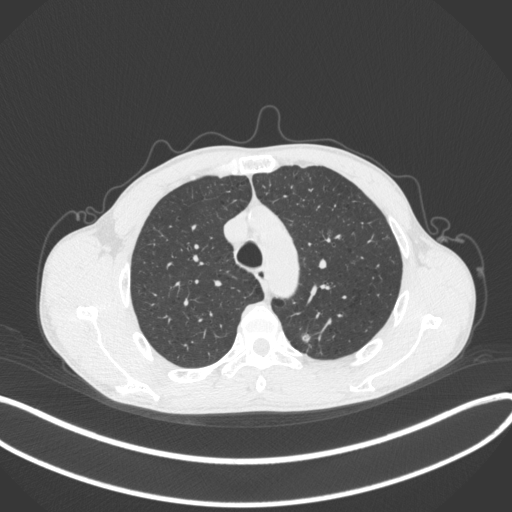
Chest CT, one axial slice. Slice 304 of 429 in the series (ordered by position). Lung window (W 1500 / L -600 HU). 512 × 512 image matrix. Male patient, age 51 years. From the clinical record (not read from this slice): clinical TNM (as recorded): T2a N1 M1.
Outlined on this slice (rectangle marked by the reading radiologist):
- lung tumour (recorded histology: adenocarcinoma): box from (x=296, y=328) to (x=315, y=351) px